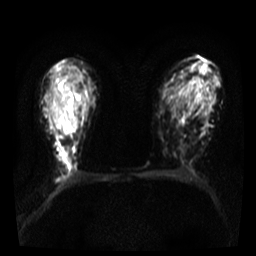
Breast MRI, one axial slice; slice 23 of 36 in the series (ordered by position); diffusion-weighted series; image 2 of 4 stored at this slice position (different b-values; order by instance number); 3 T; 256 × 256 image matrix, field of view 300 × 300 mm. Female patient.
Annotated regions visible in this slice (expert manual segmentation):
- tumour on diffusion-weighted imaging: bounding box <56,92,68,108> (left, top, right, bottom; pixels)